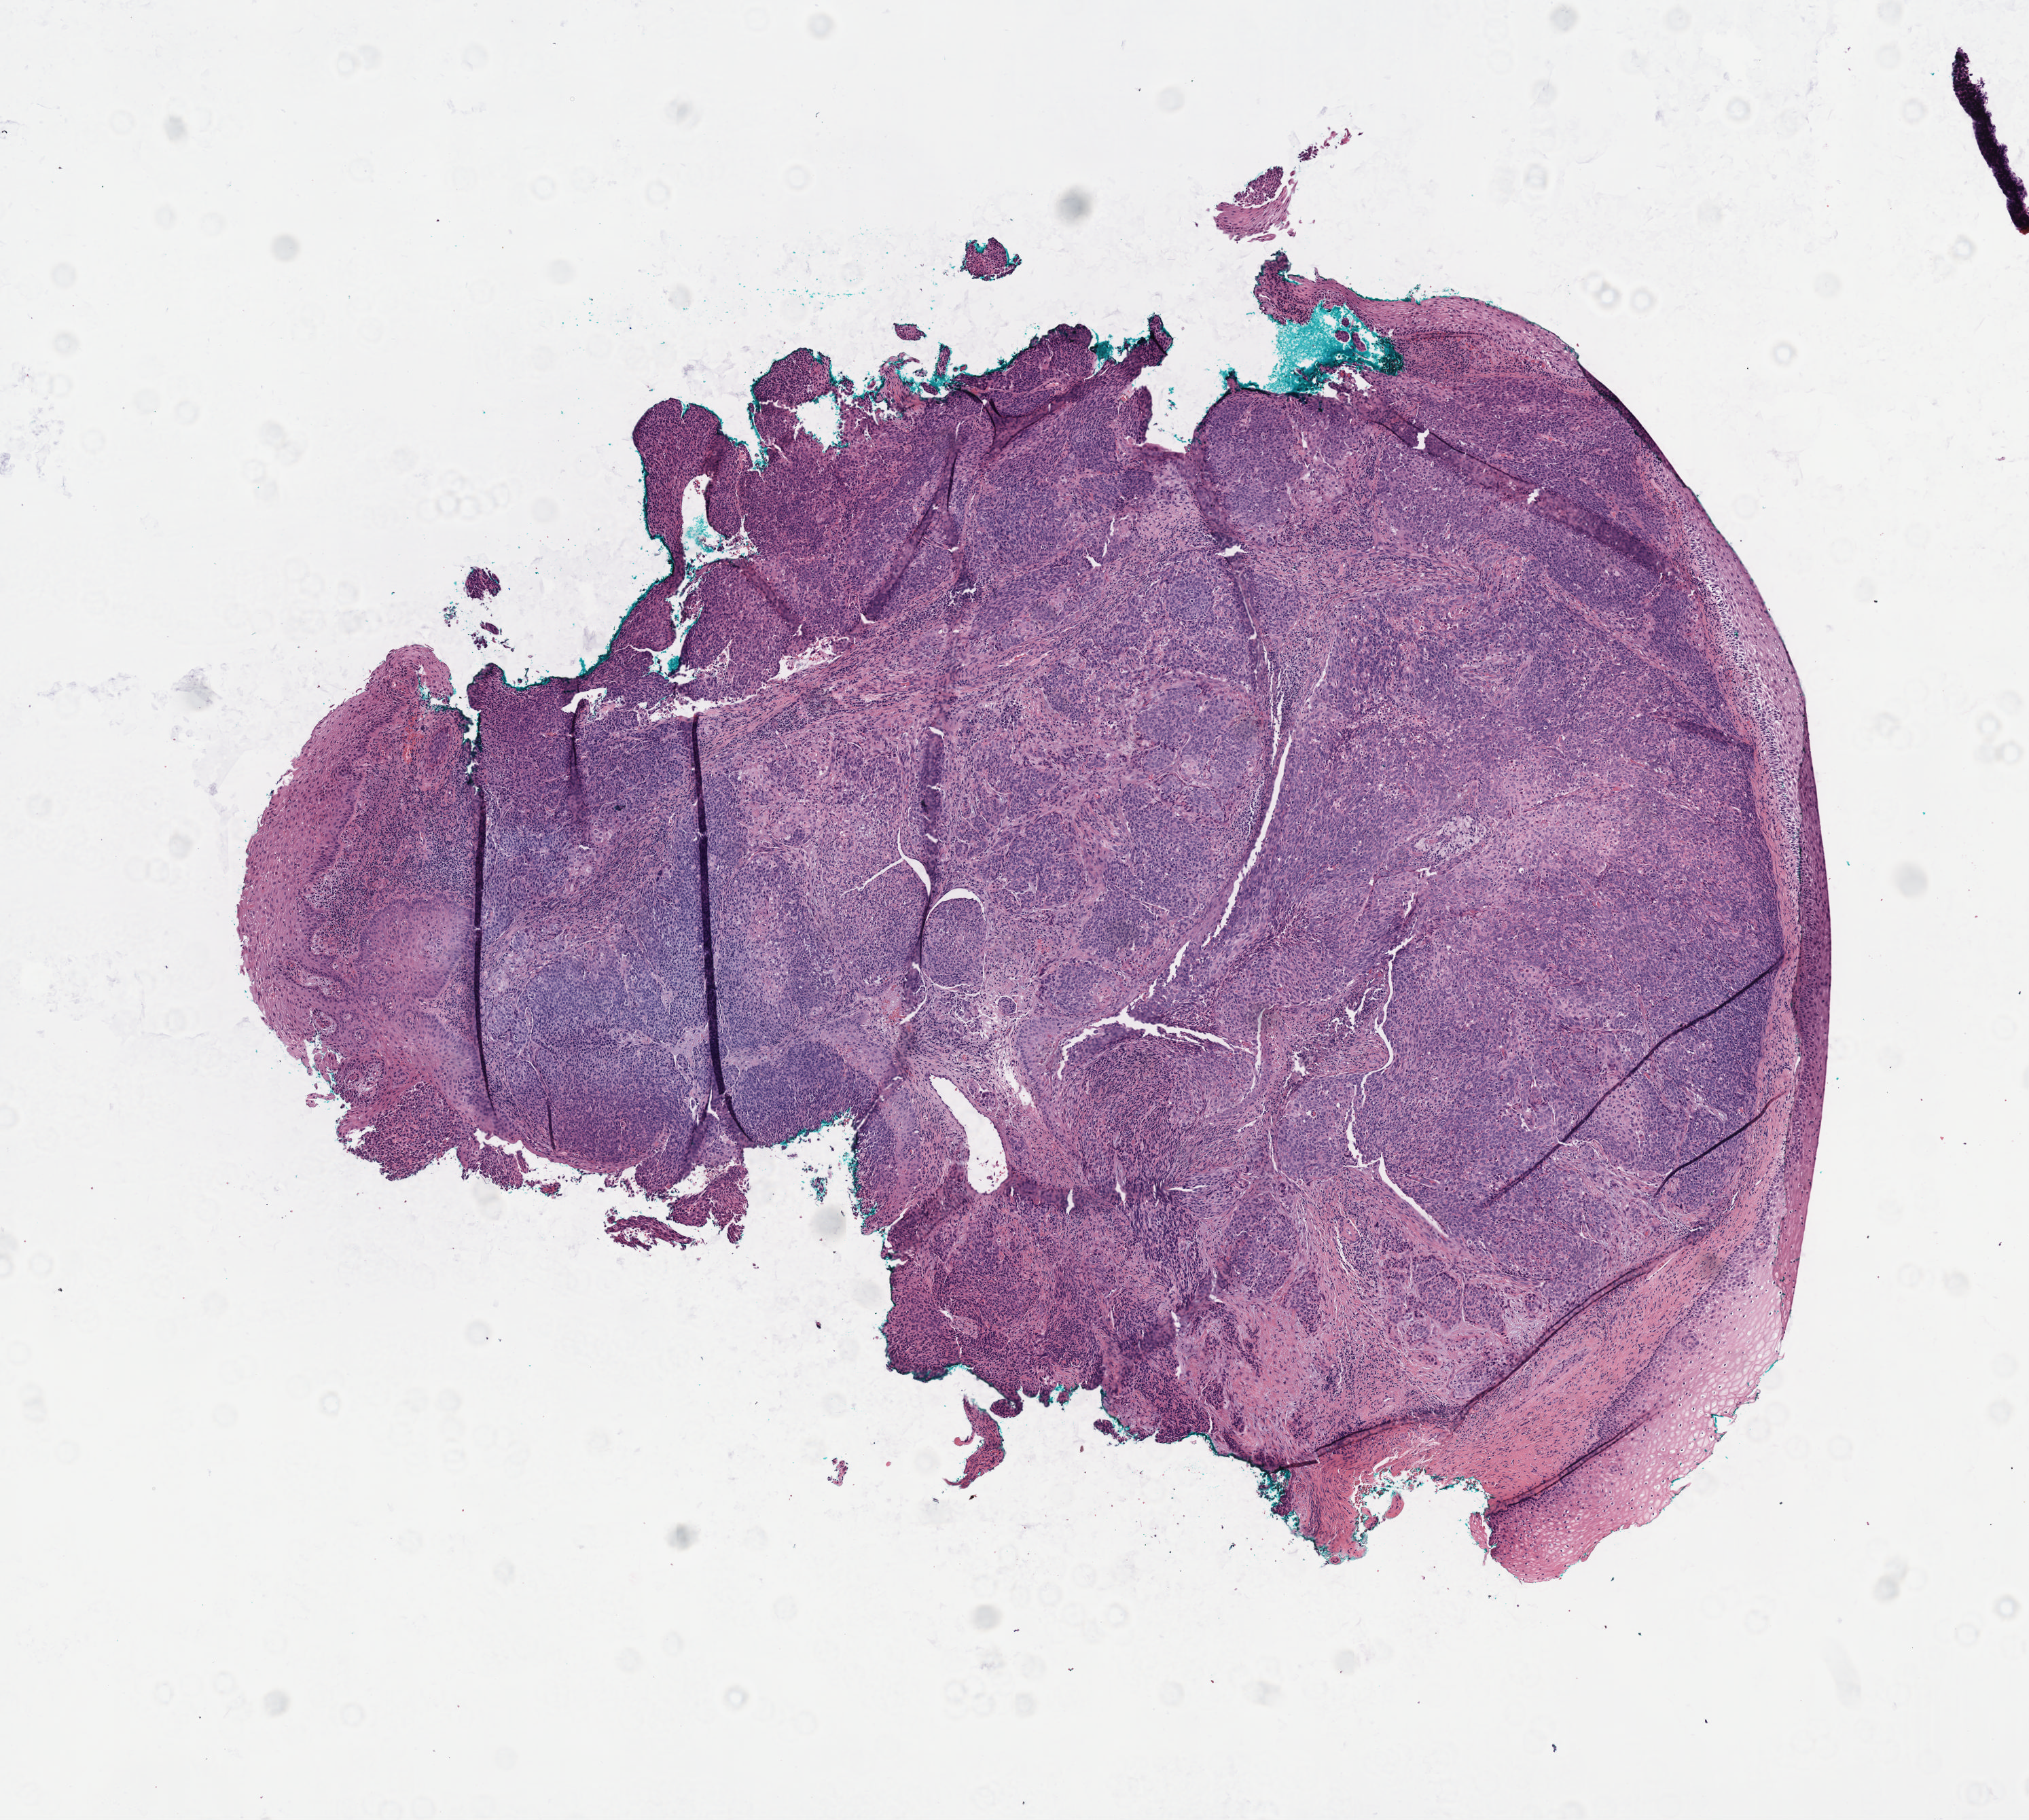
Digitized H&E-stained tissue section (whole slide), a low-resolution overview of the entire scanned area, about 6.0 x 5.4 mm. Formalin-fixed paraffin-embedded (FFPE) diagnostic section. Primary tumour sample from the cervix. Patient: female, age at initial diagnosis 39 years. Histologic grade: G2 (moderately differentiated).
FIGO stage: IVB. Diagnosis: Squamous cell carcinoma, NOS (cervix uteri).